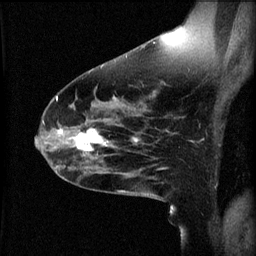
Breast MRI (dynamic contrast-enhanced), one sagittal slice. Slice 35 of 60 in the series (ordered by position). 3 images stored at this slice position (order not interpretable as contrast timing). 1.5 T. TE 4.2 ms, TR 8.2 ms. 256 × 256 image matrix. Patient: female, 49 years.
Structures marked on this image (semi-automatic segmentation, software-assisted and operator-edited):
- analysis volume of interest (the breast-tissue region the enhancement analysis was run in; not a lesion): bounding box (x1, y1, x2, y2) in pixels: (66, 124, 113, 159)
- tumour enhancement mask (voxels above the 70 % enhancement threshold inside the analysis volume of interest): (72, 130, 109, 153)